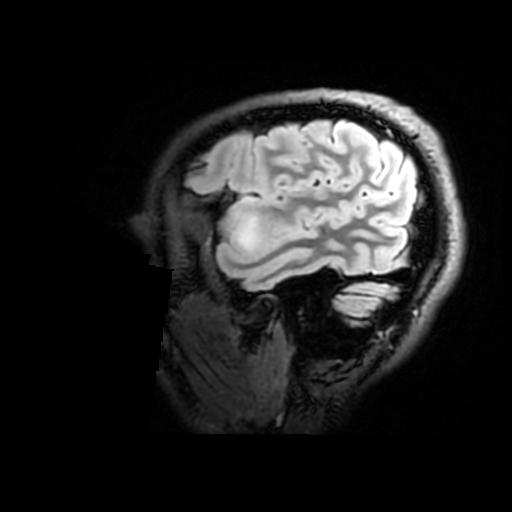
Brain MRI from a brain-tumour surgery series, one sagittal slice. Position 141 of 176 along the scan axis. T2 FLAIR. 1 mm slice thickness. 512 × 512 image matrix, field of view 240 × 240 mm. Case-level facts recorded for this patient, not image findings: histopathology: Astrocytoma; WHO grade: 2; IDH mutation: yes; tumour location: Right Insular.
Outlined on this slice (manually delineated by an expert):
- tumour: bounding box <241,195,253,249> (left, top, right, bottom; pixels)